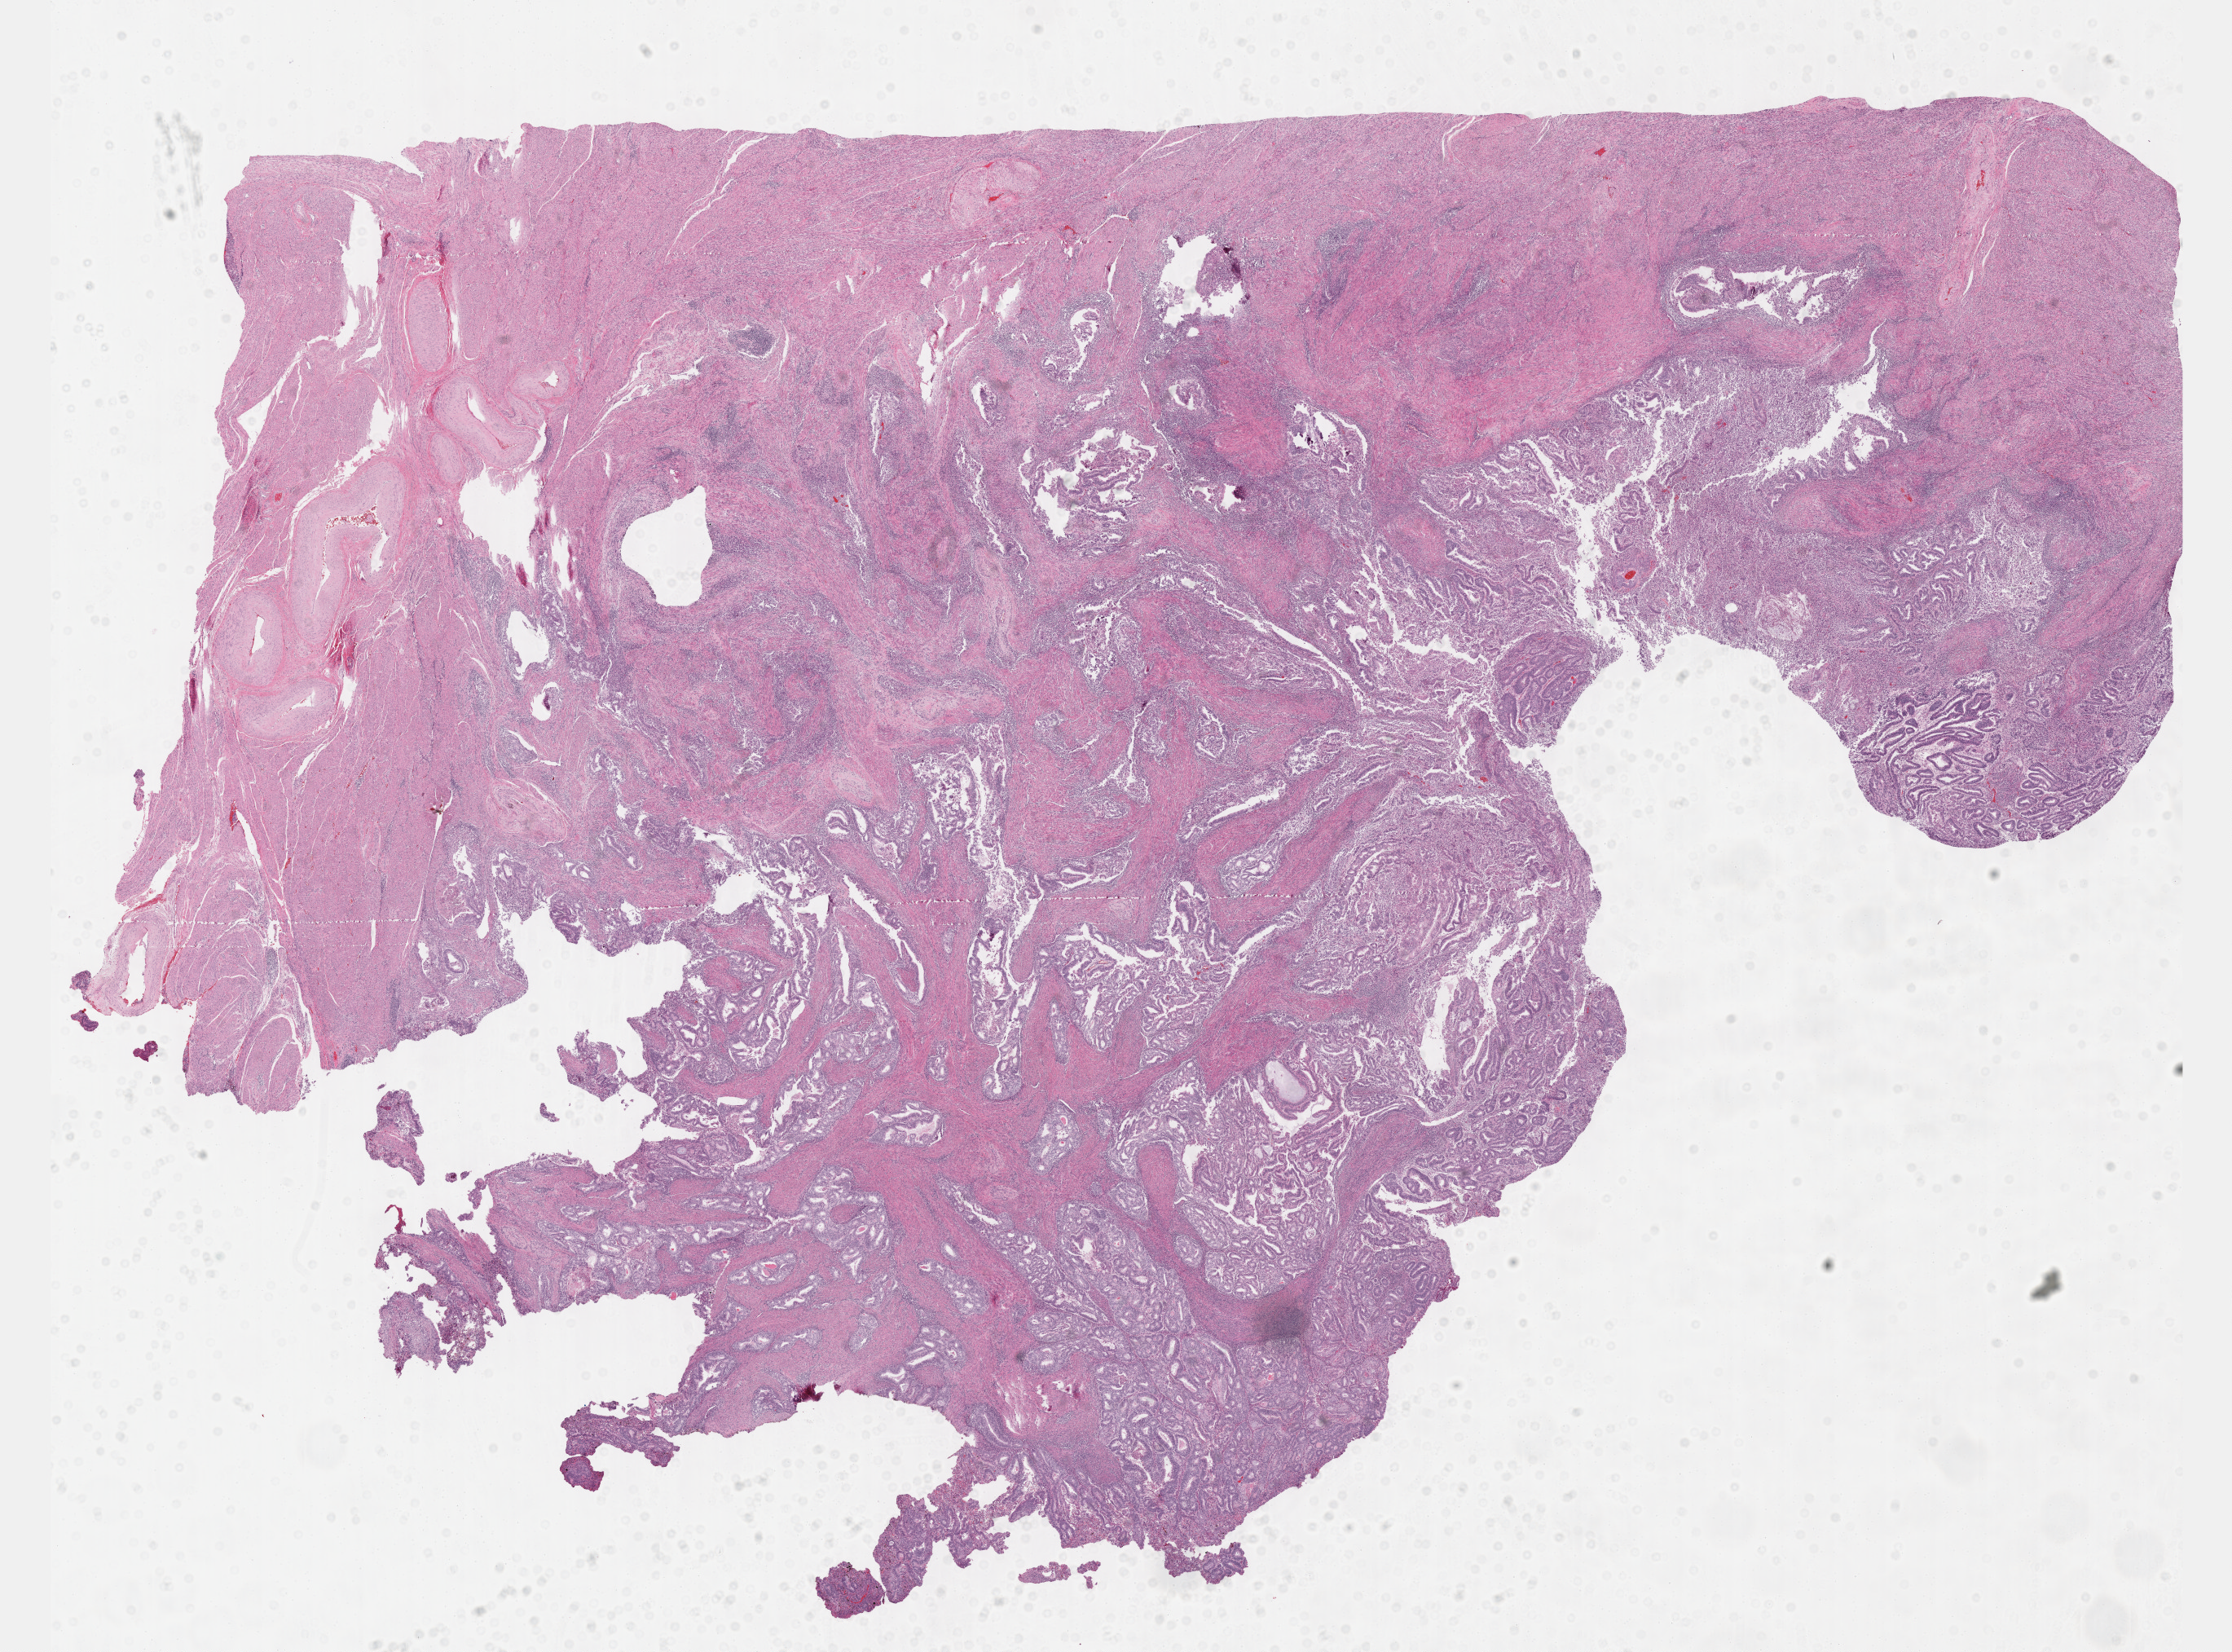
Hematoxylin and eosin (H&E) stained whole-slide image — a low-resolution overview of the entire scanned area, about 22.1 x 16.4 mm (from a 40x scan). Formalin-fixed paraffin-embedded (FFPE) diagnostic section. Uterus, primary tumour sample. Female patient; age at initial diagnosis 64 years. Histologic grade: G1 (well differentiated).
FIGO stage: IB. Diagnosis: Endometrioid adenocarcinoma, NOS (endometrium).